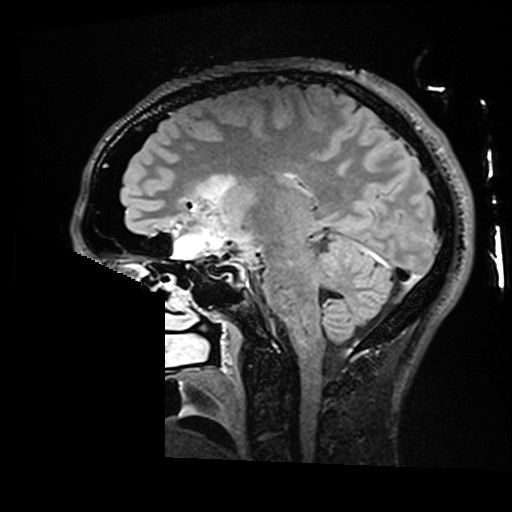
Brain MRI from a brain-tumour surgery series, one sagittal slice; T2 FLAIR; 1 mm slice thickness; 512 × 512 image matrix, field of view 250 × 250 mm. Case-level facts recorded for this patient, not image findings: histopathology: Astrocytoma; WHO grade: 2; IDH mutation: yes.
Outlined on this slice (expert manual segmentation):
- residual tumour: bounding box [x1, y1, x2, y2] px = [198, 175, 235, 203]